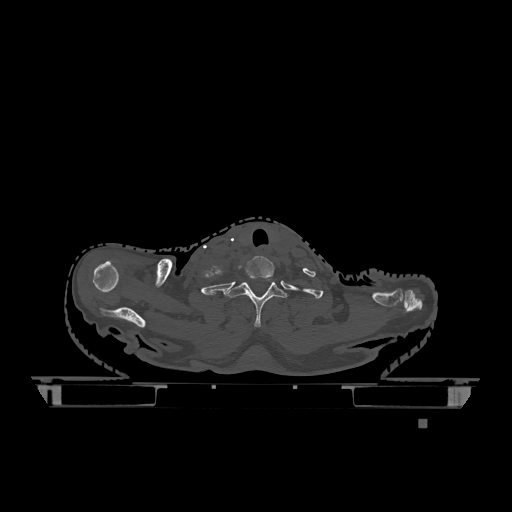
CT including the spine, one axial slice. Slice 1006 of 1317 in the series (ordered by position). Bone window (W 1800 / L 400 HU). 0.5 mm slice thickness. 512 × 512 image matrix, field of view 500 × 500 mm. Patient: female, 74 years. From the clinical record (not read from this slice): primary cancer: lung; vertebrae with lytic lesions (as recorded): T1, T4, T5, T6, L4, L5.
Structures marked on this image (semi-automatically segmented with operator editing):
- T1 vertebra: bounding box <224,277,287,327> (left, top, right, bottom; pixels)